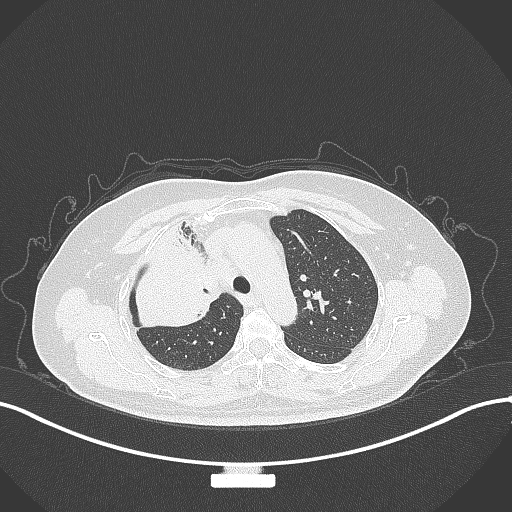
Chest CT, one axial slice. Position 224 of 309 along the scan axis. Reconstruction kernel B70f. Lung window (W 1500 / L -600 HU). 1 mm slice thickness. 512 × 512 image matrix. Patient: female, 60 years. From the clinical record (not read from this slice): clinical TNM (as recorded): T3 N1 M1.
Structures marked on this image (bounding box drawn by a radiologist):
- lung tumour (recorded histology: adenocarcinoma): box from (x=133, y=225) to (x=225, y=336) px